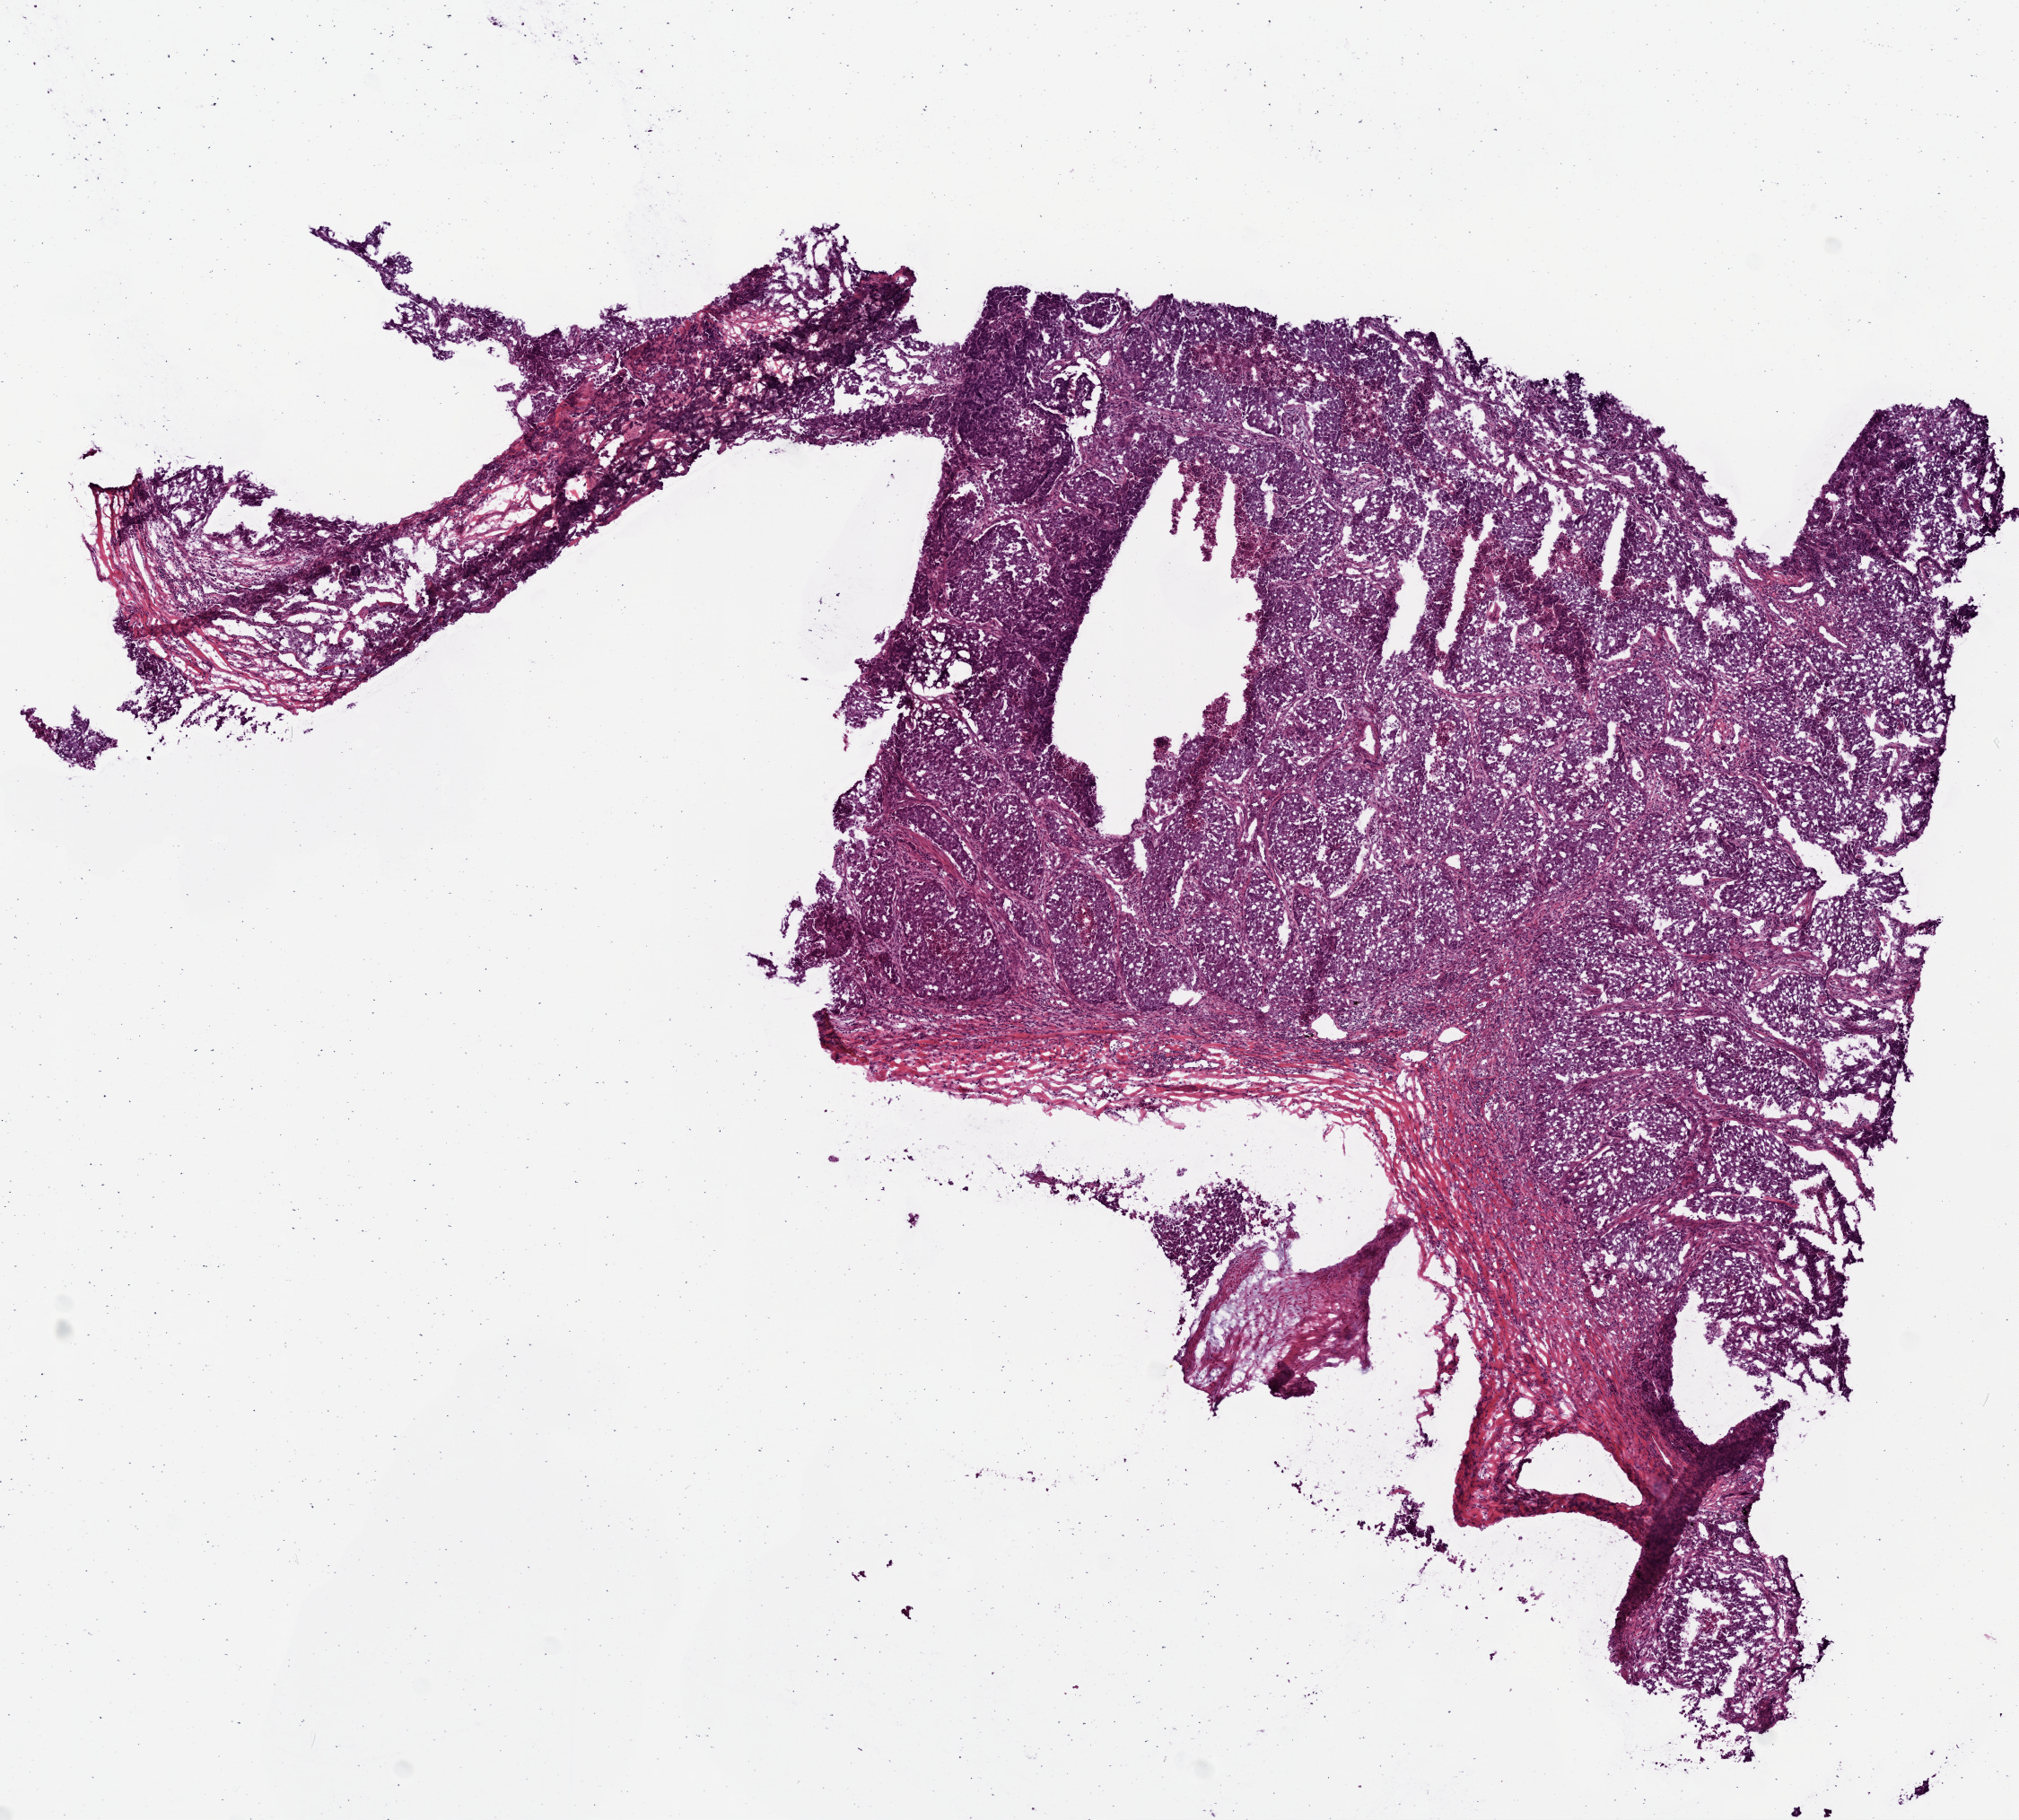
Whole-slide histology image, H&E-stained, a low-resolution overview of the entire scanned area, about 9.0 x 8.1 mm (from a 20x scan), frozen section from the top of the tissue portion, primary tumour sample from the lung. Male, age 67 years at initial diagnosis. Composition of this section per pathologist review: tumour cells 85%, tumour nuclei 80%, normal cells 0%, stromal cells 15%, necrosis 0%.
Histologic diagnosis: Adenocarcinoma, NOS (middle lobe, lung). AJCC pathologic stage: IIA (7th edition).